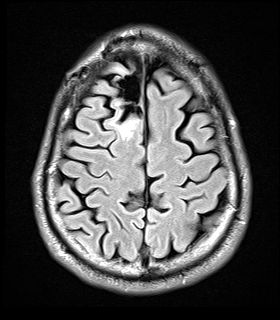
Brain MRI from a brain-tumour surgery series, one axial slice. Slice 7 of 32 in the series (ordered by position). T2 FLAIR. 280 × 320 image matrix. From the clinical record (not read from this slice): histopathology: Glial fibroma; tumour location: Right Frontal.
Structures marked on this image (manually delineated by an expert):
- tumour: bounding box <104,65,137,140> (left, top, right, bottom; pixels)